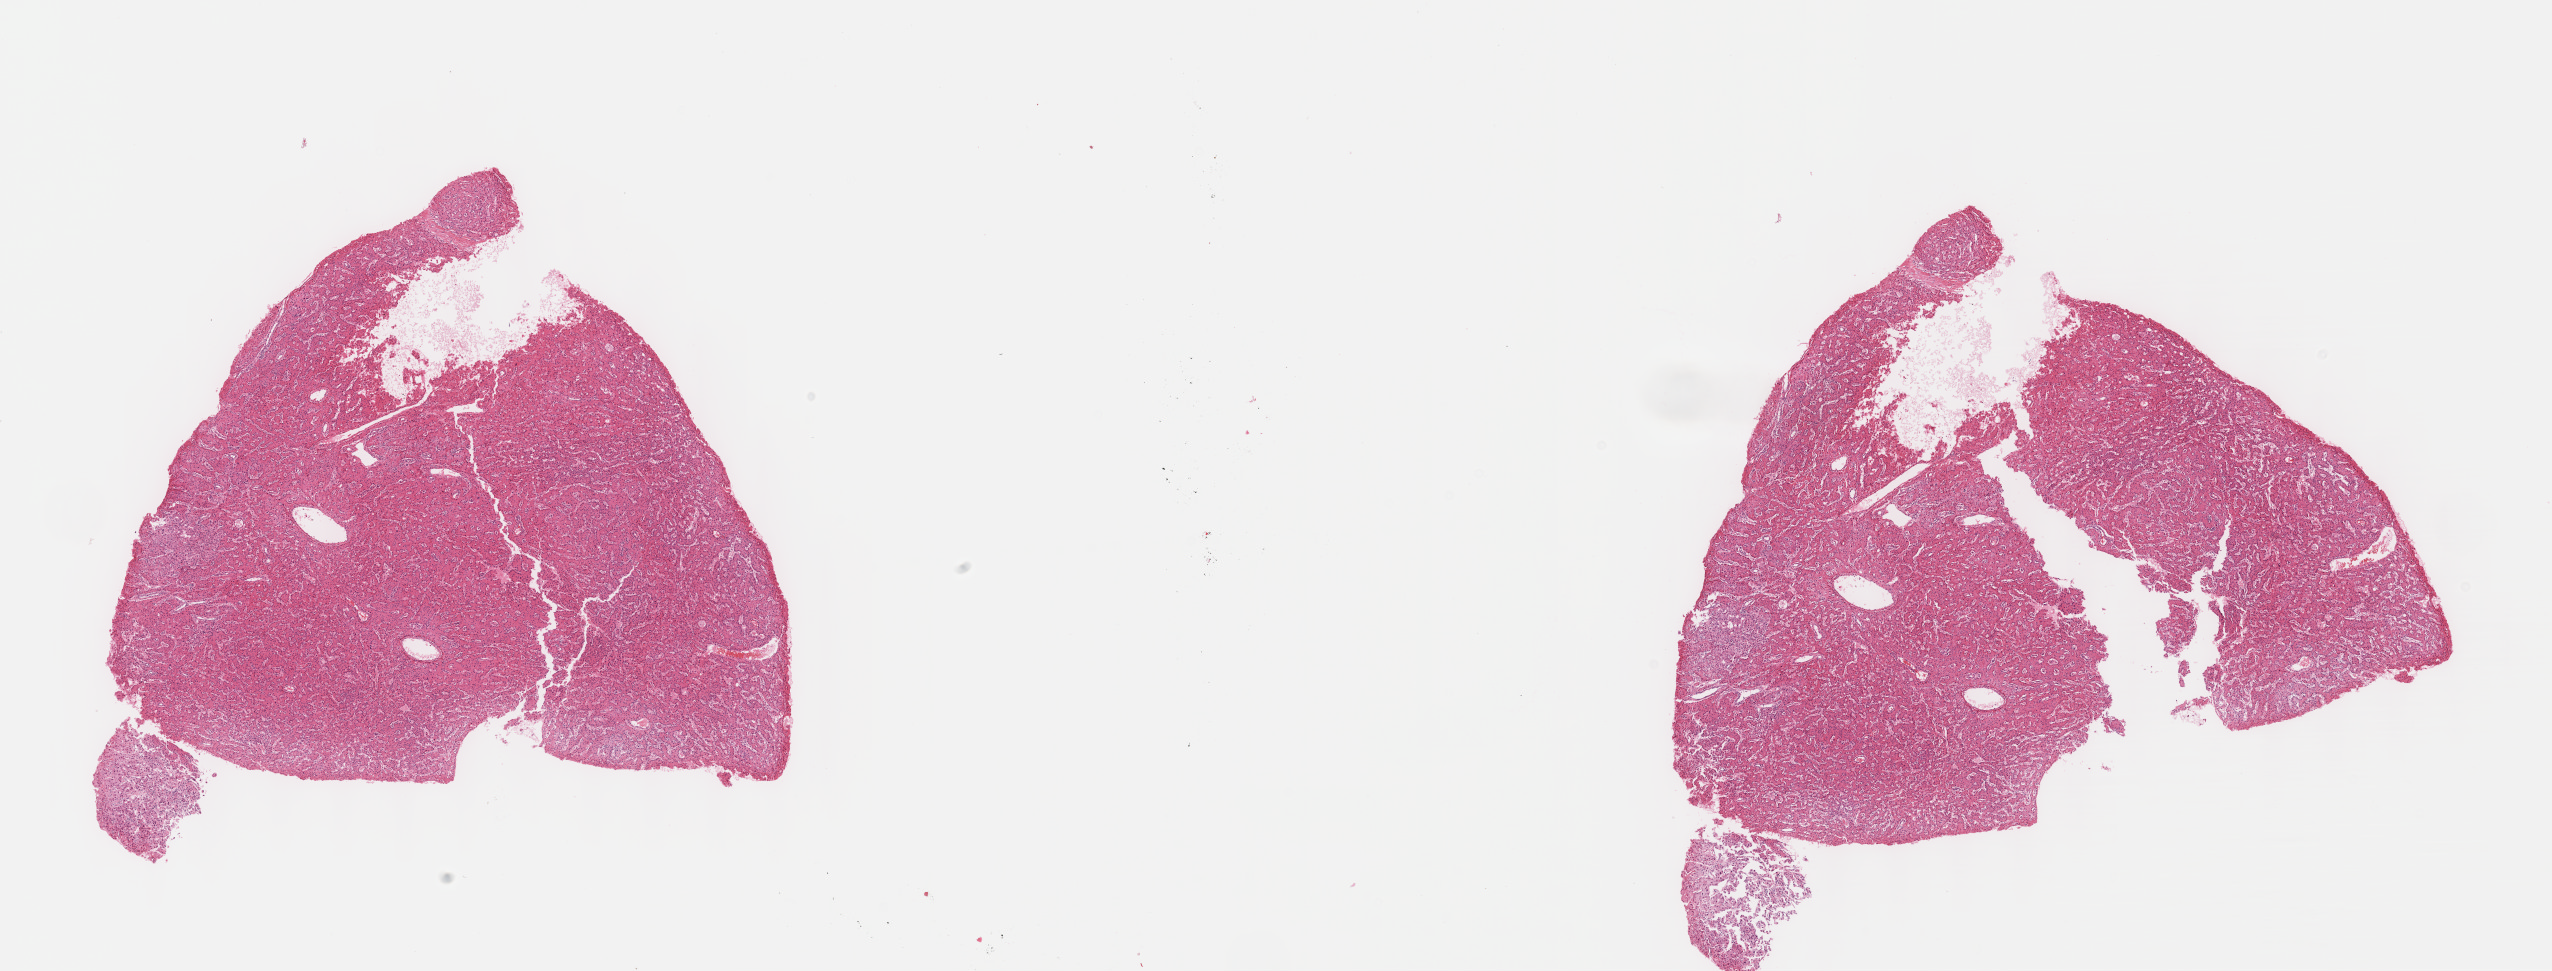
Digitized H&E-stained tissue section (whole slide), a low-resolution overview of the entire scanned area, about 20.6 x 7.8 mm (acquisition: 40x scan). FFPE section. Liver, primary tumour sample. Male patient; age at initial diagnosis 50 years. Histologic grade: G3 (poorly differentiated).
AJCC pathologic stage: I (7th edition). Pathologic diagnosis: Hepatocellular carcinoma, NOS.